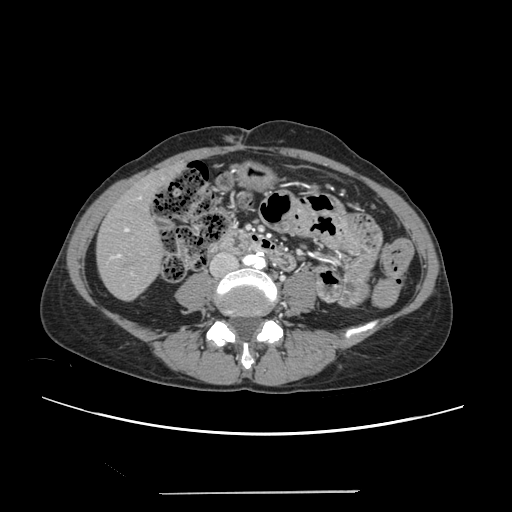
Contrast-enhanced abdominal CT, one axial slice; slice 52 of 240 in the series (ordered by position); 120 kVp; intravenous contrast given; soft-tissue window (W 400 / L 40 HU); 1.25 mm slice thickness; 512 × 512 image matrix, field of view 371 × 371 mm. Female patient, age 60 years. From the clinical record (not read from this slice): diagnosis: colorectal cancer liver metastases, imaged before liver resection; multiple liver metastases: no; largest metastasis: 1.5 cm; chemotherapy before resection: yes.
Structures marked on this image (outlined manually by an expert reader):
- liver: box from (x=97, y=168) to (x=177, y=300) px
- planned liver remnant (the part of the liver to remain after resection): (x=97, y=171)–(x=170, y=300)
- portal vein (with intrahepatic branches): (x=110, y=196)–(x=142, y=274)